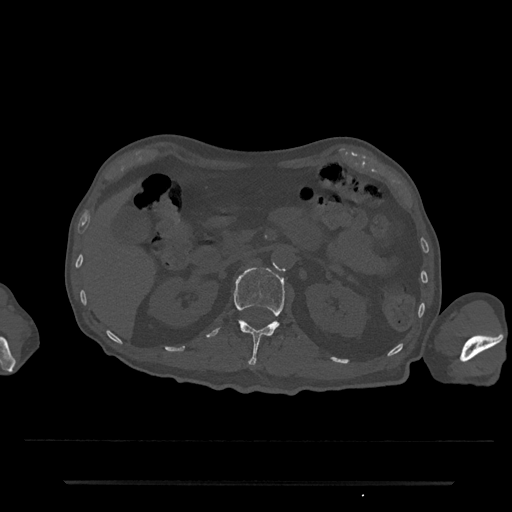
CT including the spine, one axial slice; position 125 of 797 along the scan axis; 120 kVp; bone window (W 1800 / L 400 HU); 0.5 mm slice thickness; 512 × 512 image matrix, field of view 427 × 427 mm. Patient: male, 74 years. From the clinical record (not read from this slice): primary cancer: prostate.
Outlined on this slice (semi-automatically segmented with operator editing):
- L1 vertebra: box from (x=206, y=268) to (x=300, y=365) px